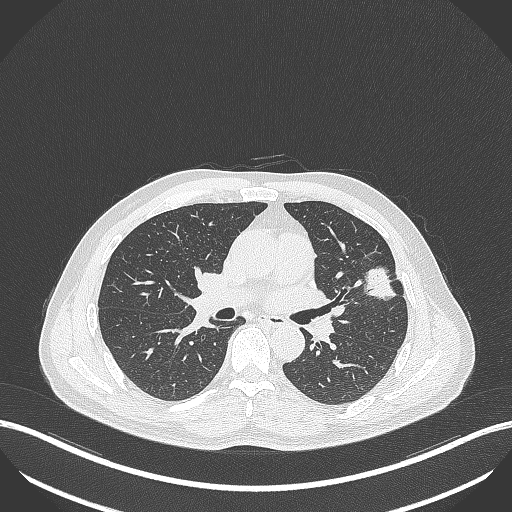
Chest CT, one axial slice. Position 222 of 418 along the scan axis. Lung window (W 1500 / L -600 HU). 512 × 512 image matrix. Male patient, age 55 years. From the clinical record (not read from this slice): clinical TNM (as recorded): T1c N0 M0.
Outlined on this slice (rectangle marked by the reading radiologist):
- lung tumour (recorded histology: adenocarcinoma): box from (x=359, y=264) to (x=397, y=301) px